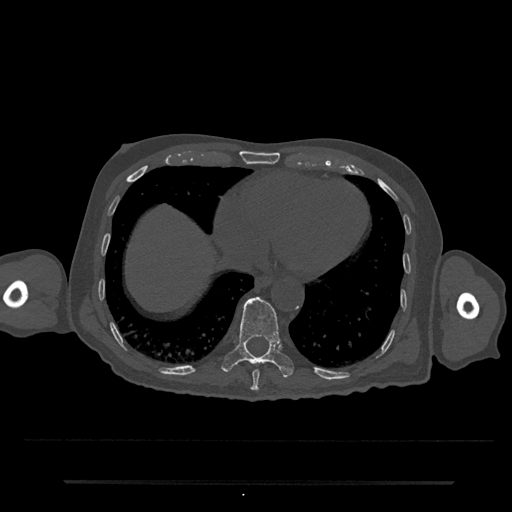
CT including the spine, one axial slice. Position 323 of 797 along the scan axis. Reconstruction kernel Br40s/3. 120 kVp. Bone window (W 1800 / L 400 HU). 0.5 mm slice thickness. 512 × 512 image matrix, field of view 427 × 427 mm. Patient: male, 74 years. From the clinical record (not read from this slice): primary cancer: prostate.
Structures marked on this image (semi-automatically segmented with operator editing):
- T10 vertebra: box from (x=221, y=297) to (x=294, y=378) px
- T9 vertebra: (x=250, y=369)–(x=260, y=391)